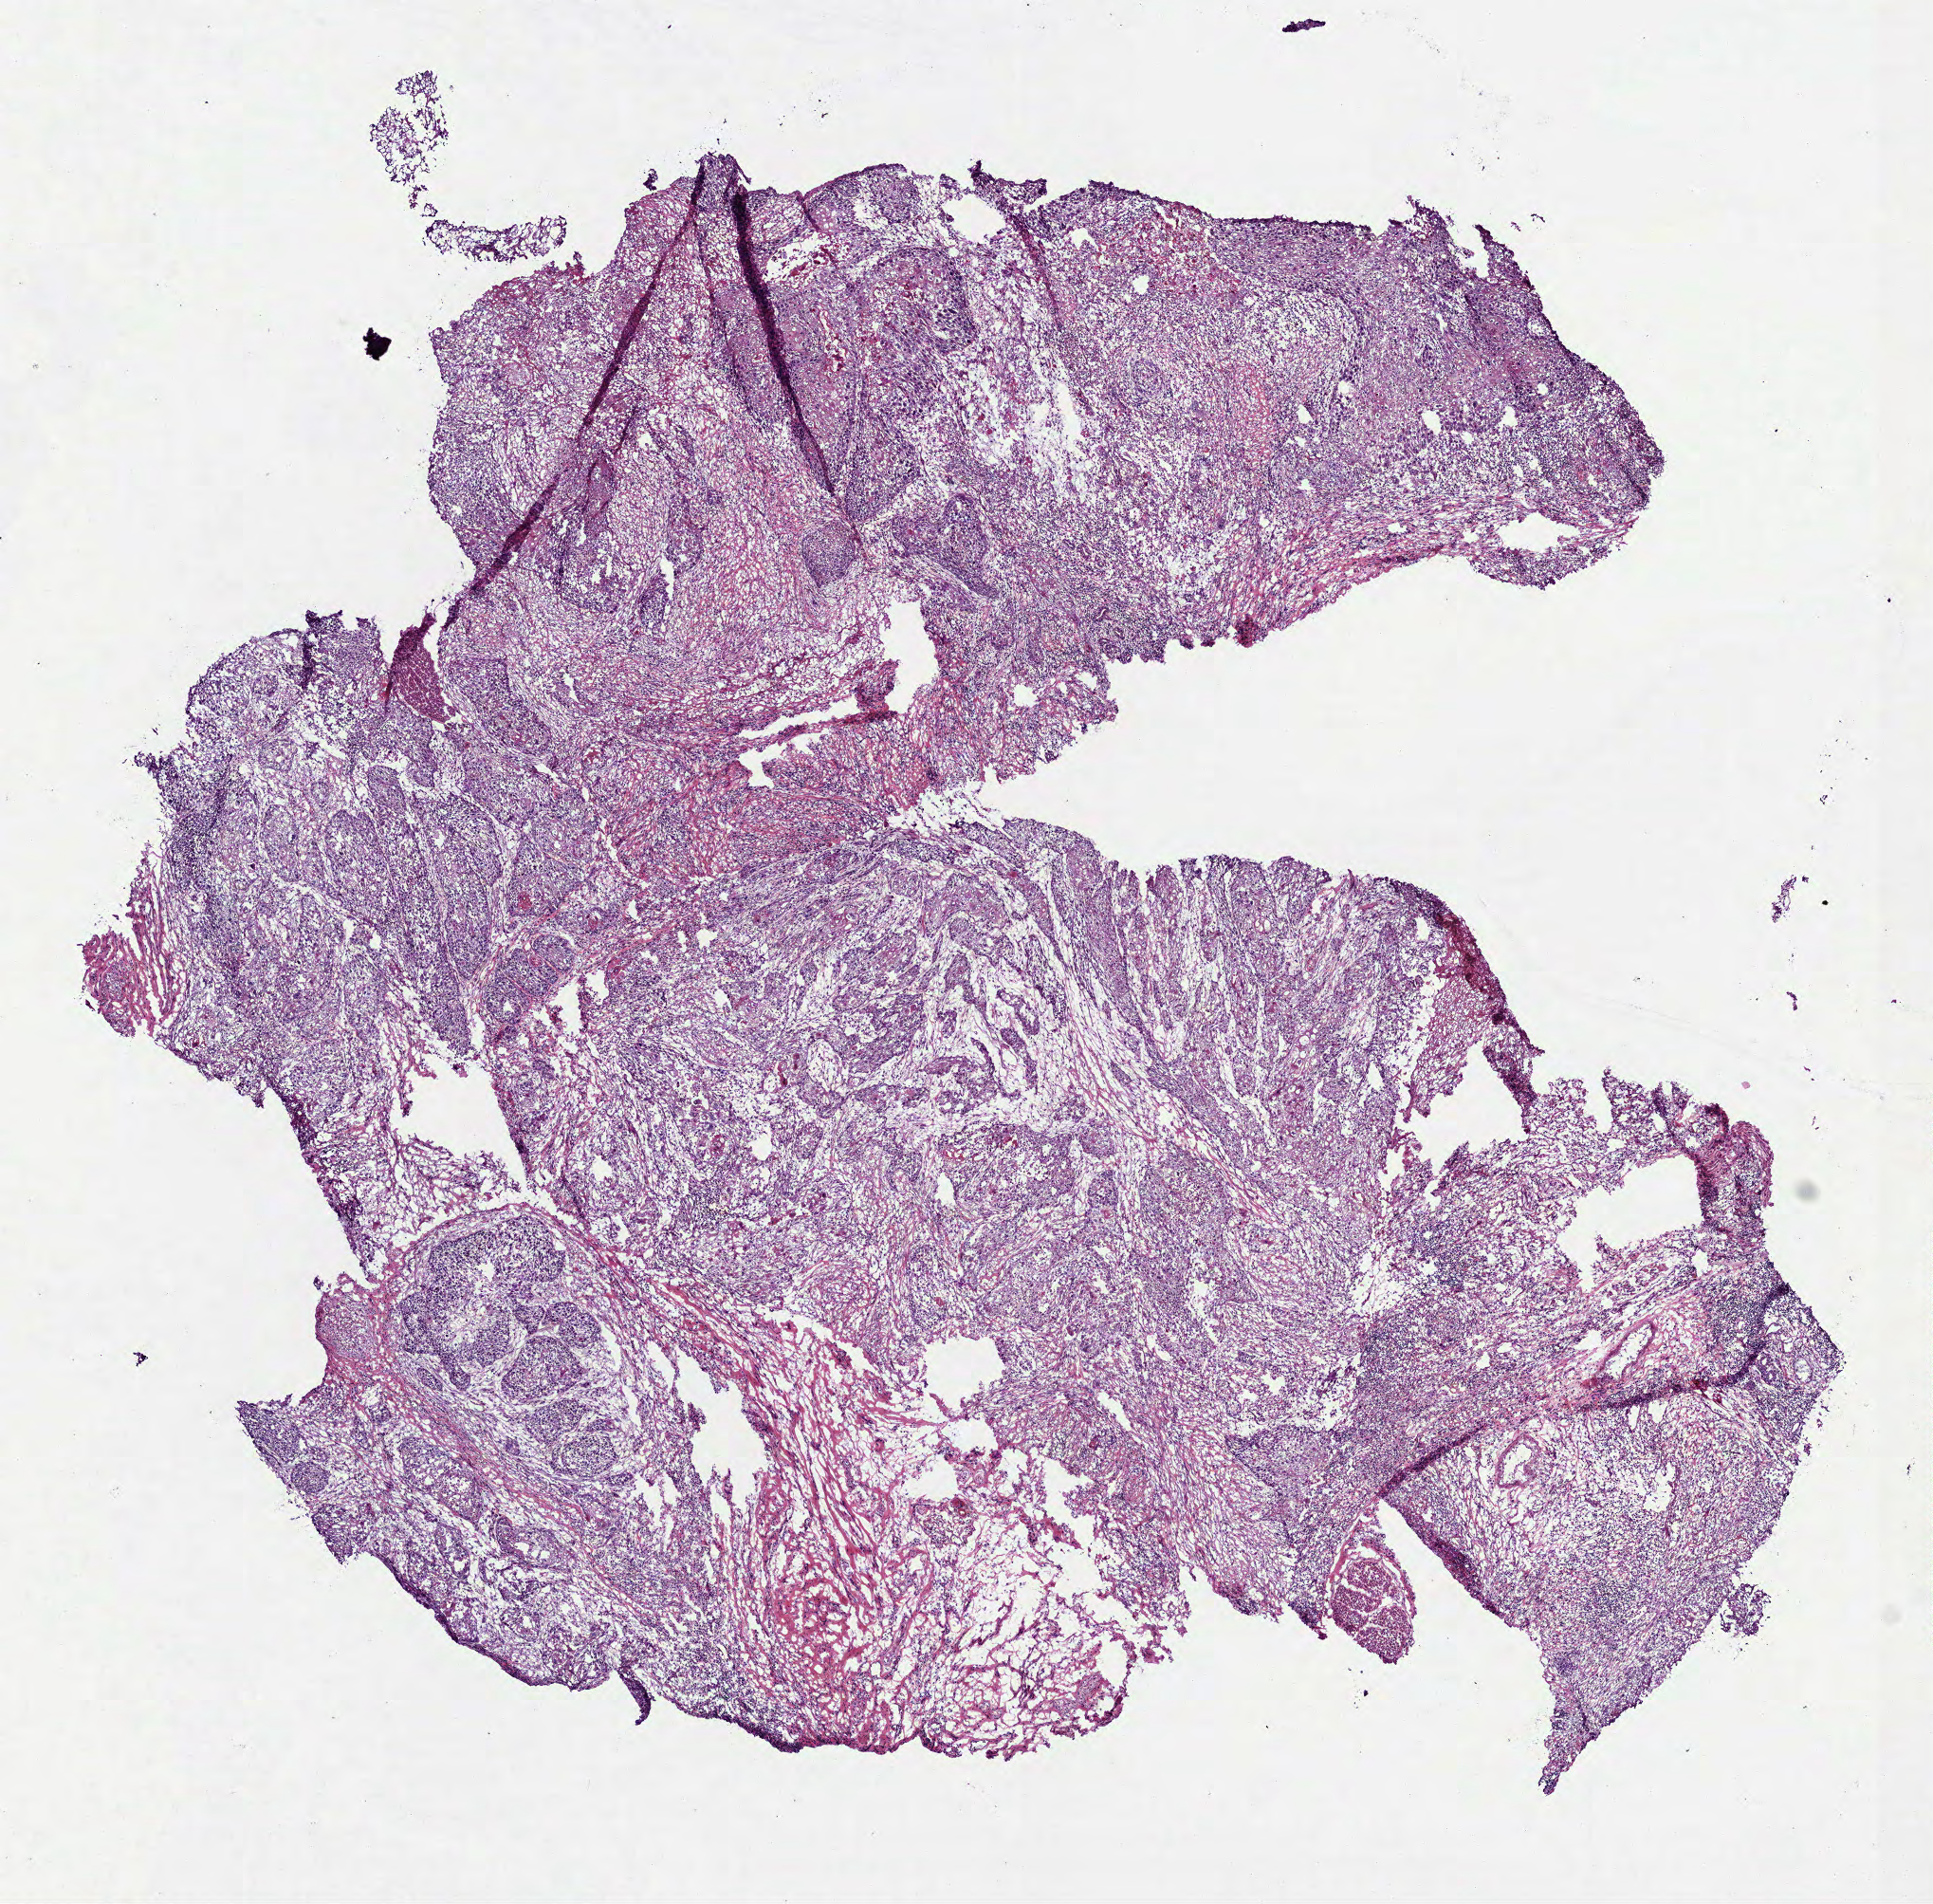
Whole-slide histology image, H&E — shown as a low-resolution overview of the whole scanned area (about 8.2 x 8.1 mm); frozen section from the top of the tissue portion; sample: primary tumour, head and neck. Male, age 58 years at initial diagnosis.
Diagnosis: Squamous cell carcinoma, NOS (floor of mouth, NOS).